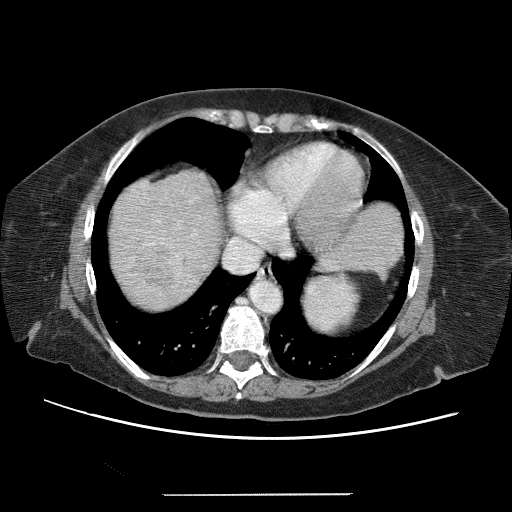
Contrast-enhanced abdominal CT (liver protocol), one axial slice; slice 56 of 65 in the series (ordered by position); reconstruction kernel STANDARD; soft-tissue window (W 400 / L 40 HU); 2.5 mm slice thickness; 512 × 512 image matrix, field of view 380 × 380 mm. Case-level facts recorded for this patient, not image findings: diagnosis: hepatocellular carcinoma (patient treated with transarterial chemoembolisation; whether this scan precedes or follows treatment is not stated here); TNM stage (as recorded): Stage-IIIB; Child-Pugh class: A; tumour differentiation: moderately differentiated.
Structures marked on this image (semi-automatic segmentation, software-assisted and operator-edited):
- abdominal aorta: box from (x=254, y=282) to (x=284, y=315) px
- liver parenchyma outside the tumour (the mass and vessels are separate outlines, so this box may not span the whole liver): (x=112, y=170)–(x=216, y=304)
- mass: (x=123, y=240)–(x=179, y=299)
- liver vessels: (x=152, y=197)–(x=197, y=272)